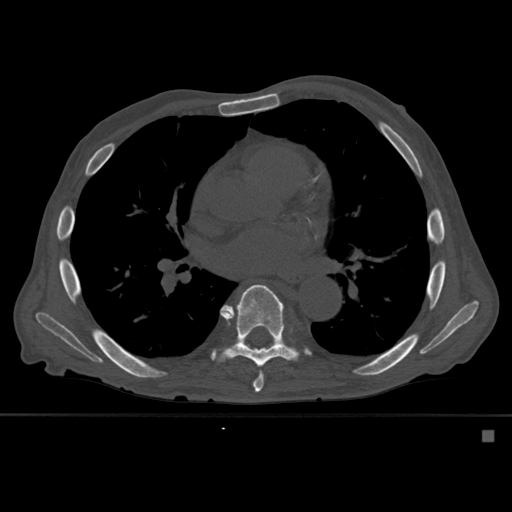
CT including the spine, one axial slice; position 352 of 527 along the scan axis; bone window (W 1800 / L 400 HU); 1.5 mm slice thickness; 512 × 512 image matrix. Patient: male, 78 years. From the clinical record (not read from this slice): primary cancer: prostate.
Outlined on this slice (semi-automatic segmentation, software-assisted and operator-edited):
- T7 vertebra: bounding box (x1, y1, x2, y2) in pixels: (225, 291, 264, 393)
- T8 vertebra: (212, 284, 299, 371)
- T9 vertebra: (237, 337, 276, 350)